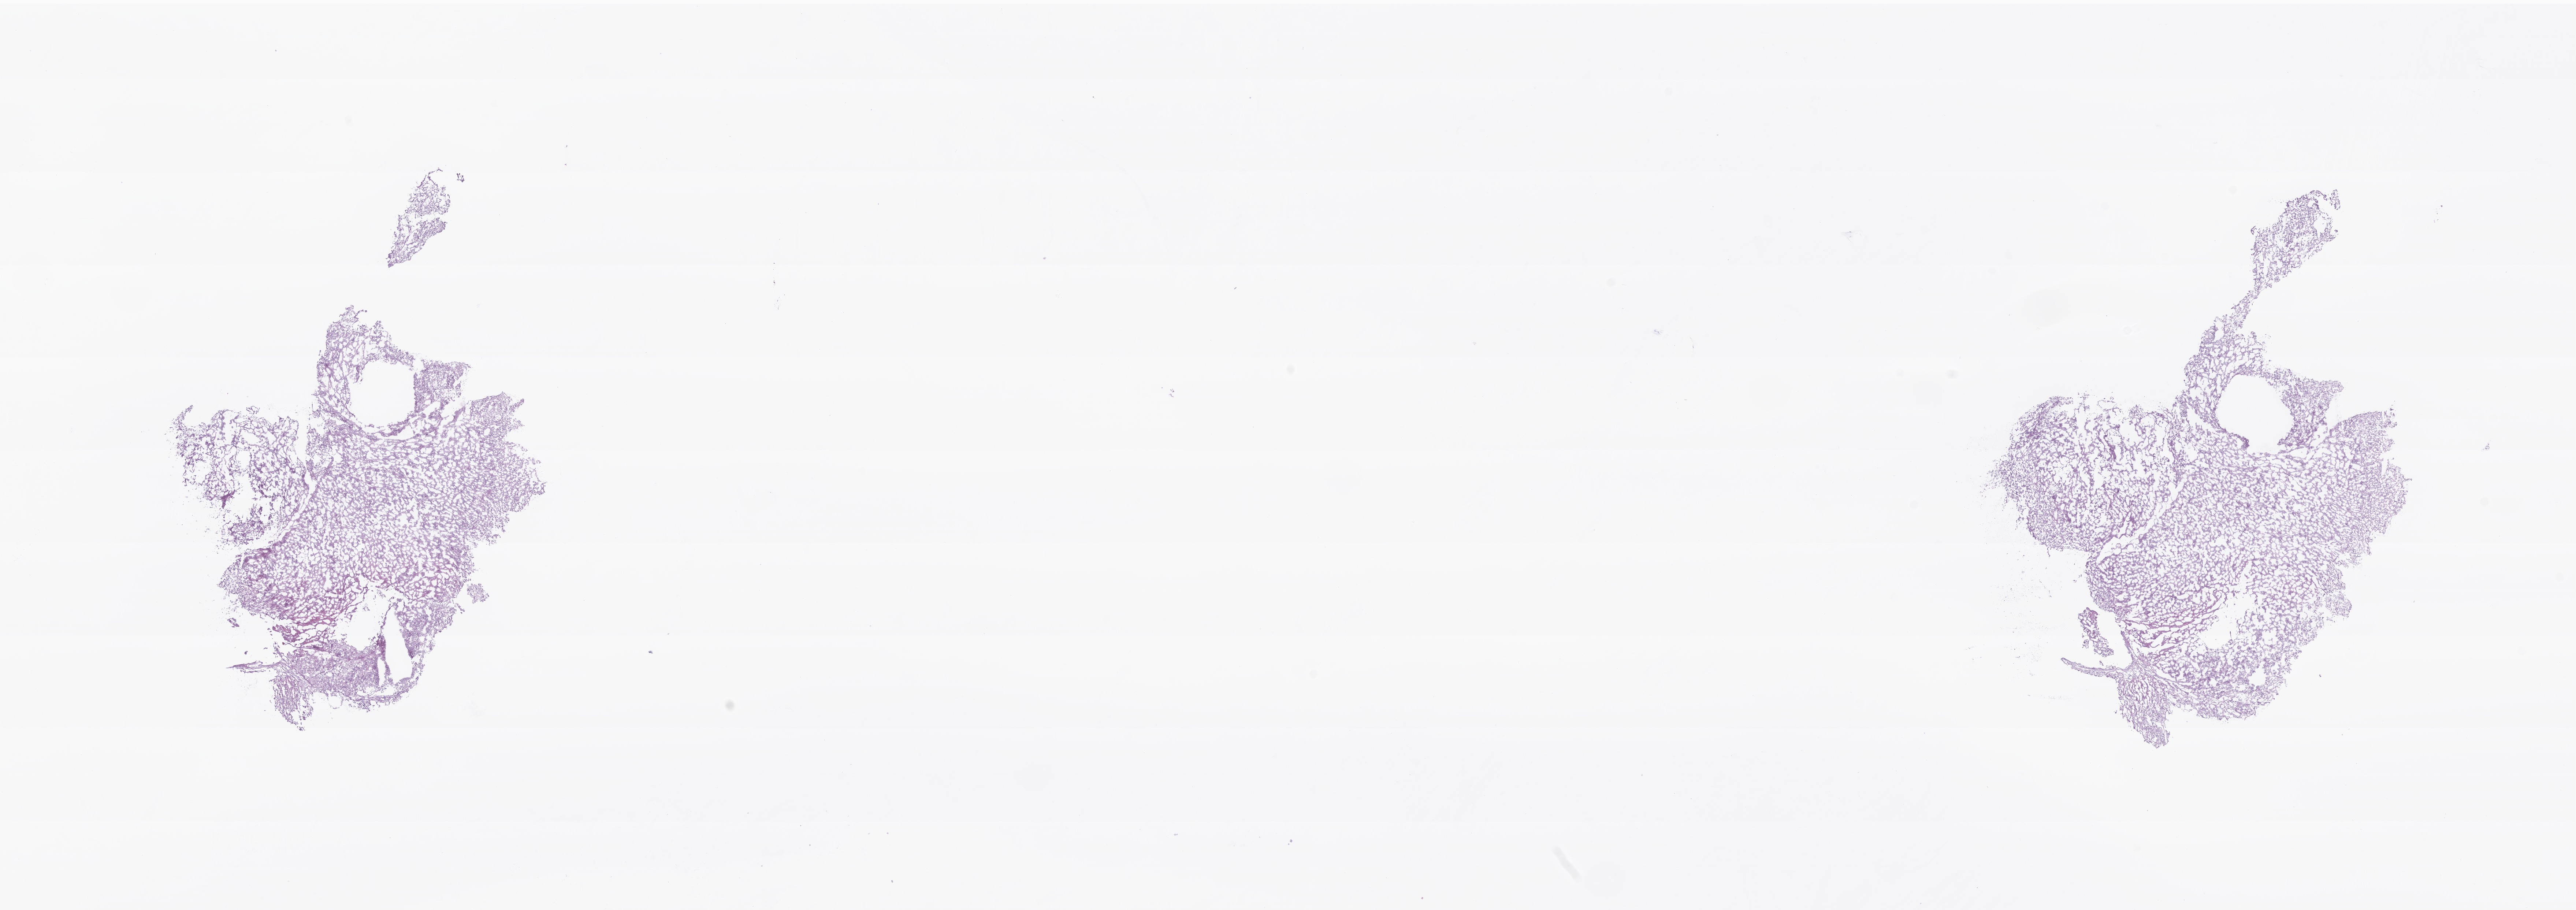
Hematoxylin and eosin (H&E) whole-slide image of tumor tissue from the brain — a low-resolution overview of the entire scanned area, about 29.6 x 10.4 mm, frozen section. Patient: male, age 650 days (about 1.8 years).
- recorded diagnosis: Ependymoma, NOS